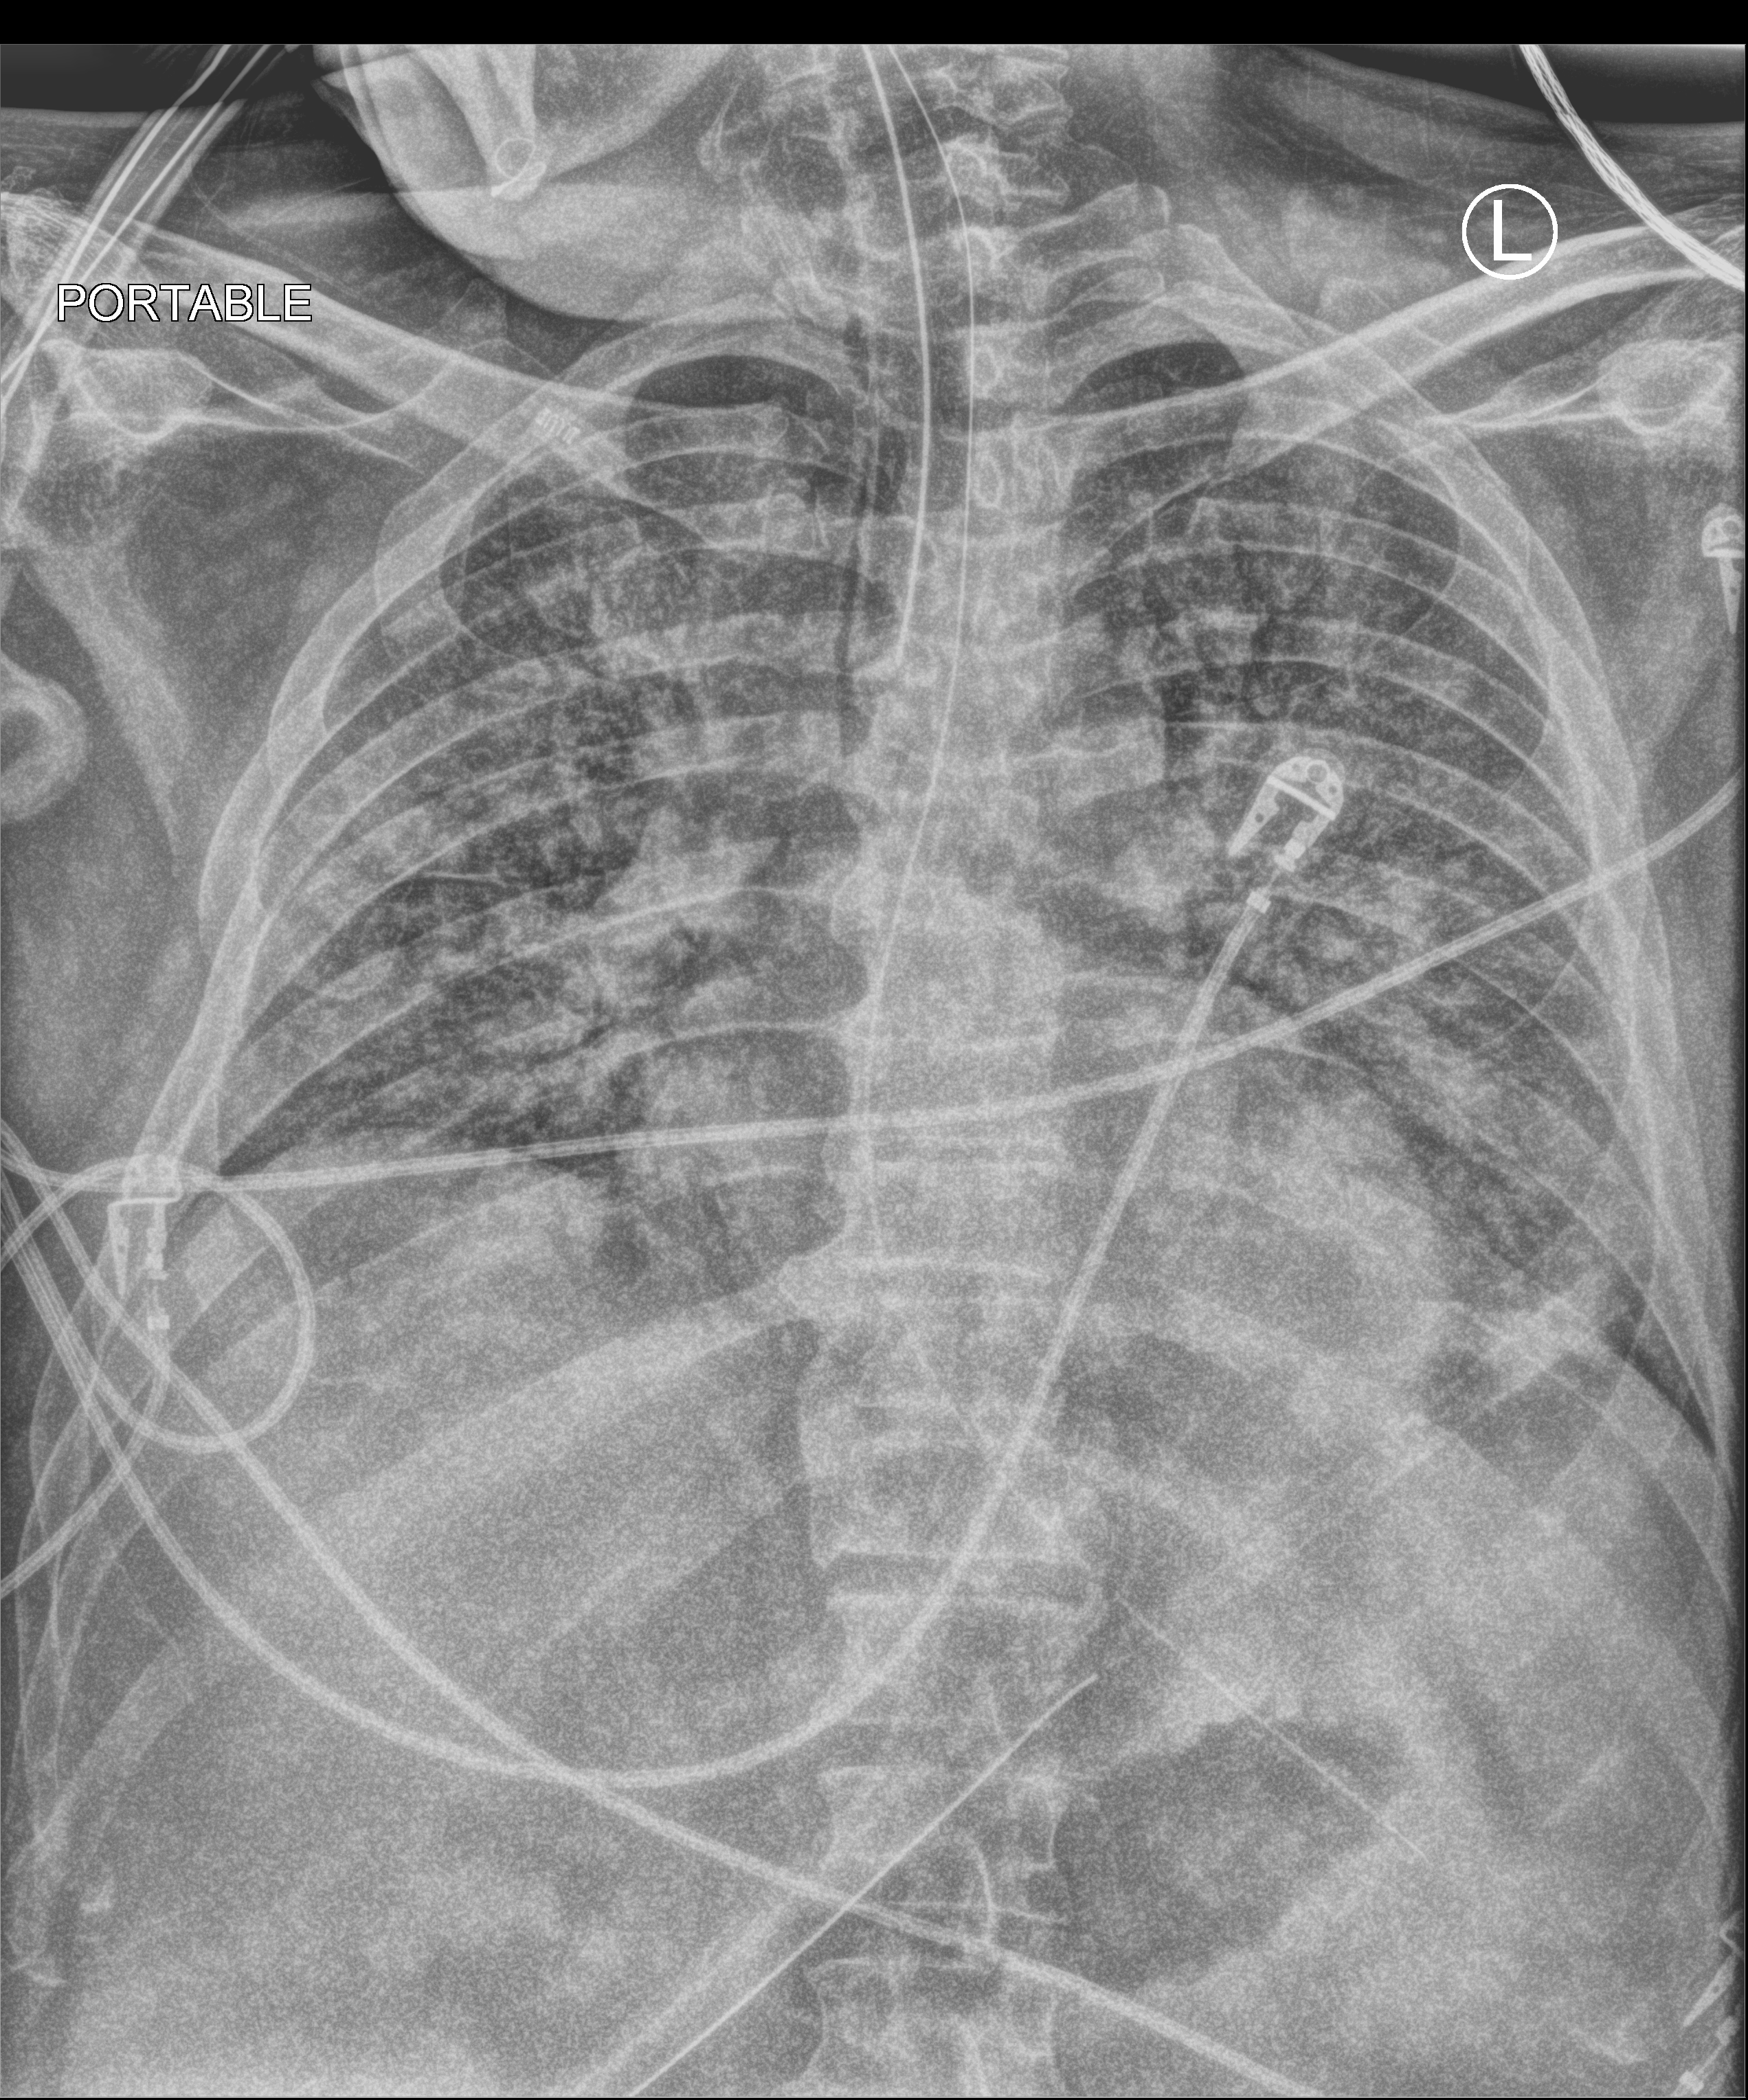
Portable chest radiograph, anteroposterior (AP) projection. Male patient hospitalised with COVID-19, age 60–74 years.
From the hospital-stay record, not from the radiograph (when in the stay this image was taken is not recorded):
- mechanically ventilated during this hospital stay: yes